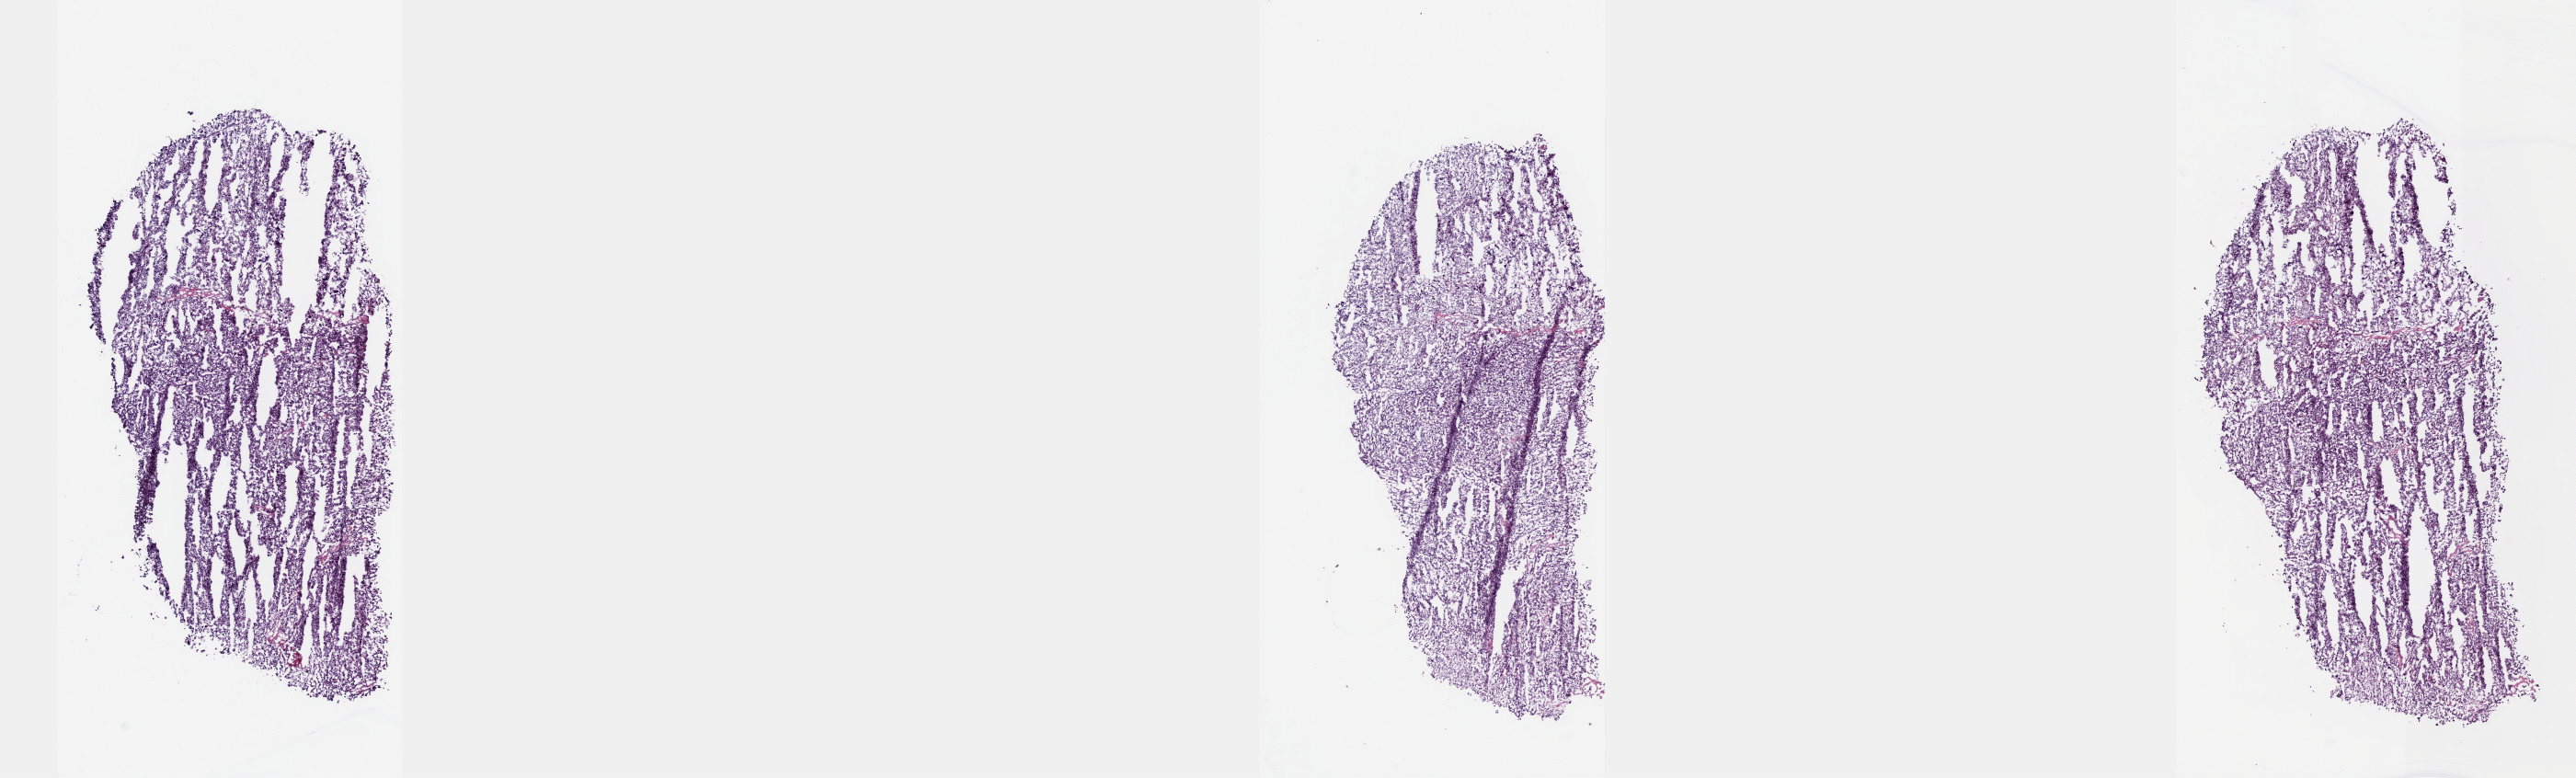
Whole-slide histology image, Hematoxylin and eosin (H&E) stained — low-resolution overview of the scanned area, about 22.6 x 6.8 mm, frozen section from the top of the tissue portion, liver, primary tumour sample. Patient: female, age at initial diagnosis 68 years. Histologic grade: G2 (moderately differentiated). Pathologist review of this section (percent, as recorded): tumour cells 80%, tumour nuclei 80%, normal cells 0%, stromal cells 20%, necrosis 0%. Inflammatory infiltration, as recorded: lymphocyte infiltration 3%, monocyte infiltration 1%, neutrophil infiltration 2%.
AJCC pathologic stage: I (7th edition). Histologic diagnosis: Clear cell adenocarcinoma, NOS.